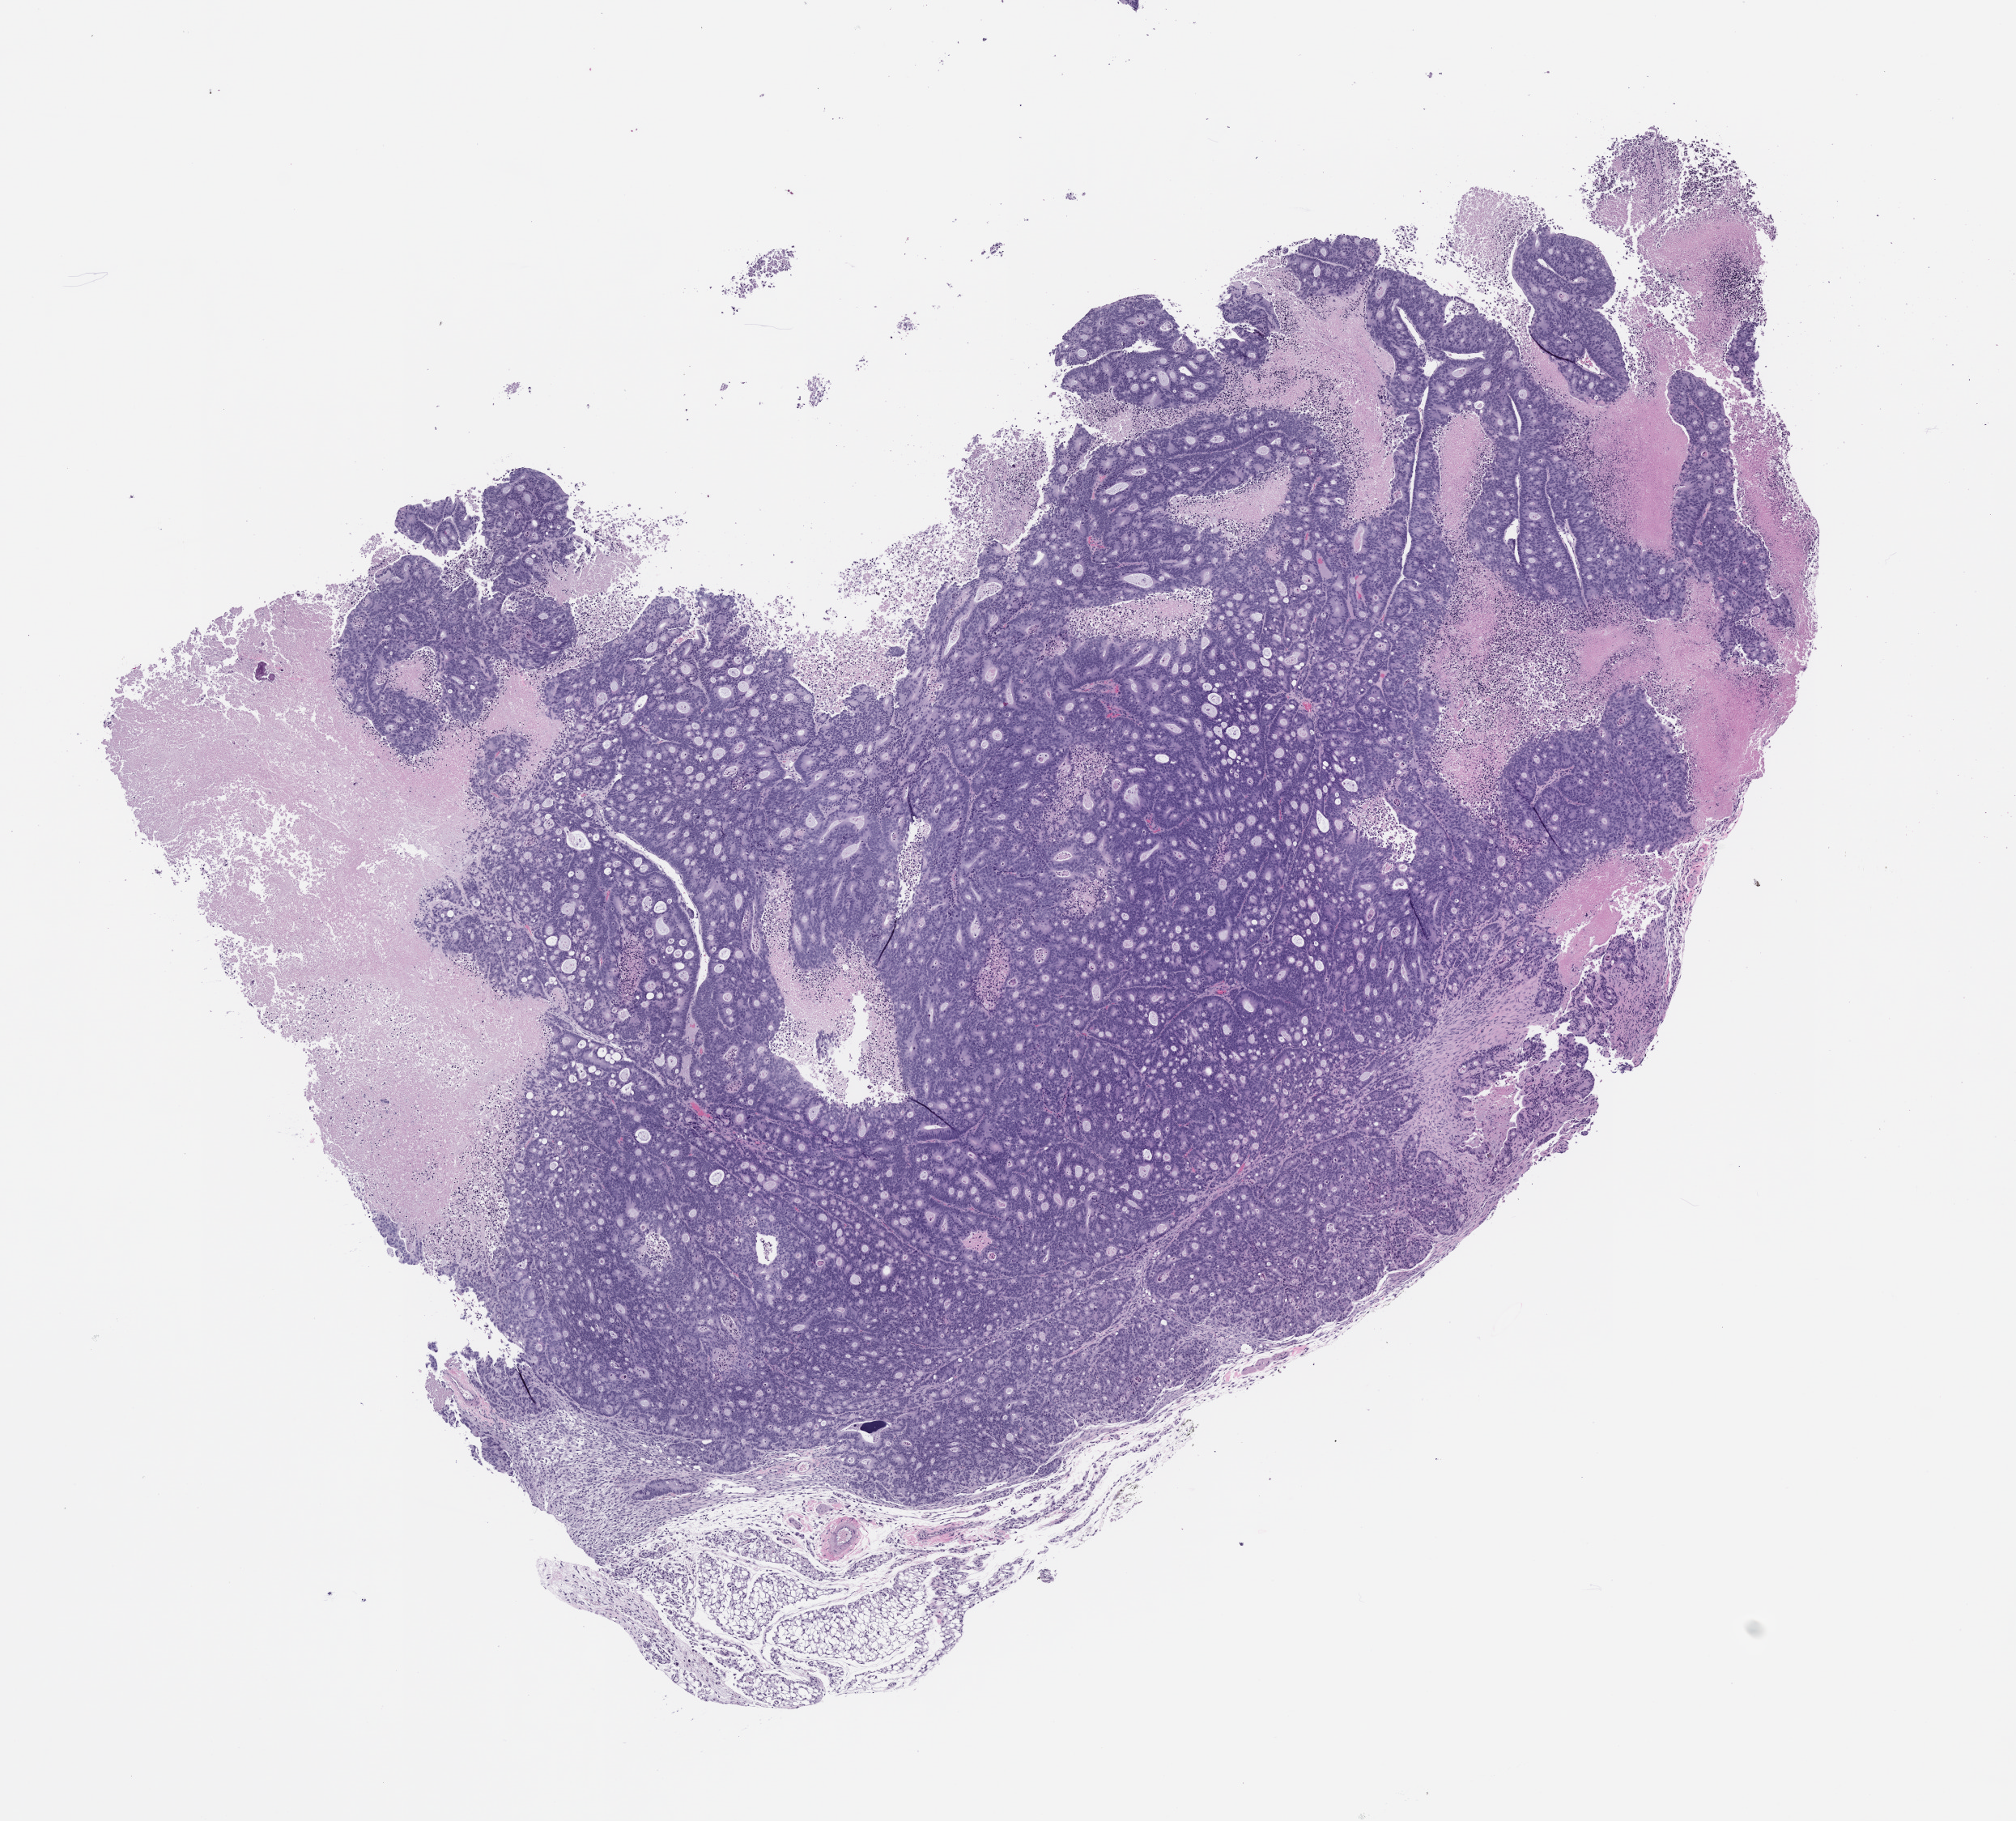
H&E whole-slide image of a patient-derived xenograft (PDX) tumor grown in a mouse, passage 3, a low-resolution overview of the entire scanned area, about 10.0 x 9.0 mm. Formalin-fixed paraffin-embedded section. Originating tumor site category: colon.
Originating patient diagnosis: Colon Adenocarcinoma.